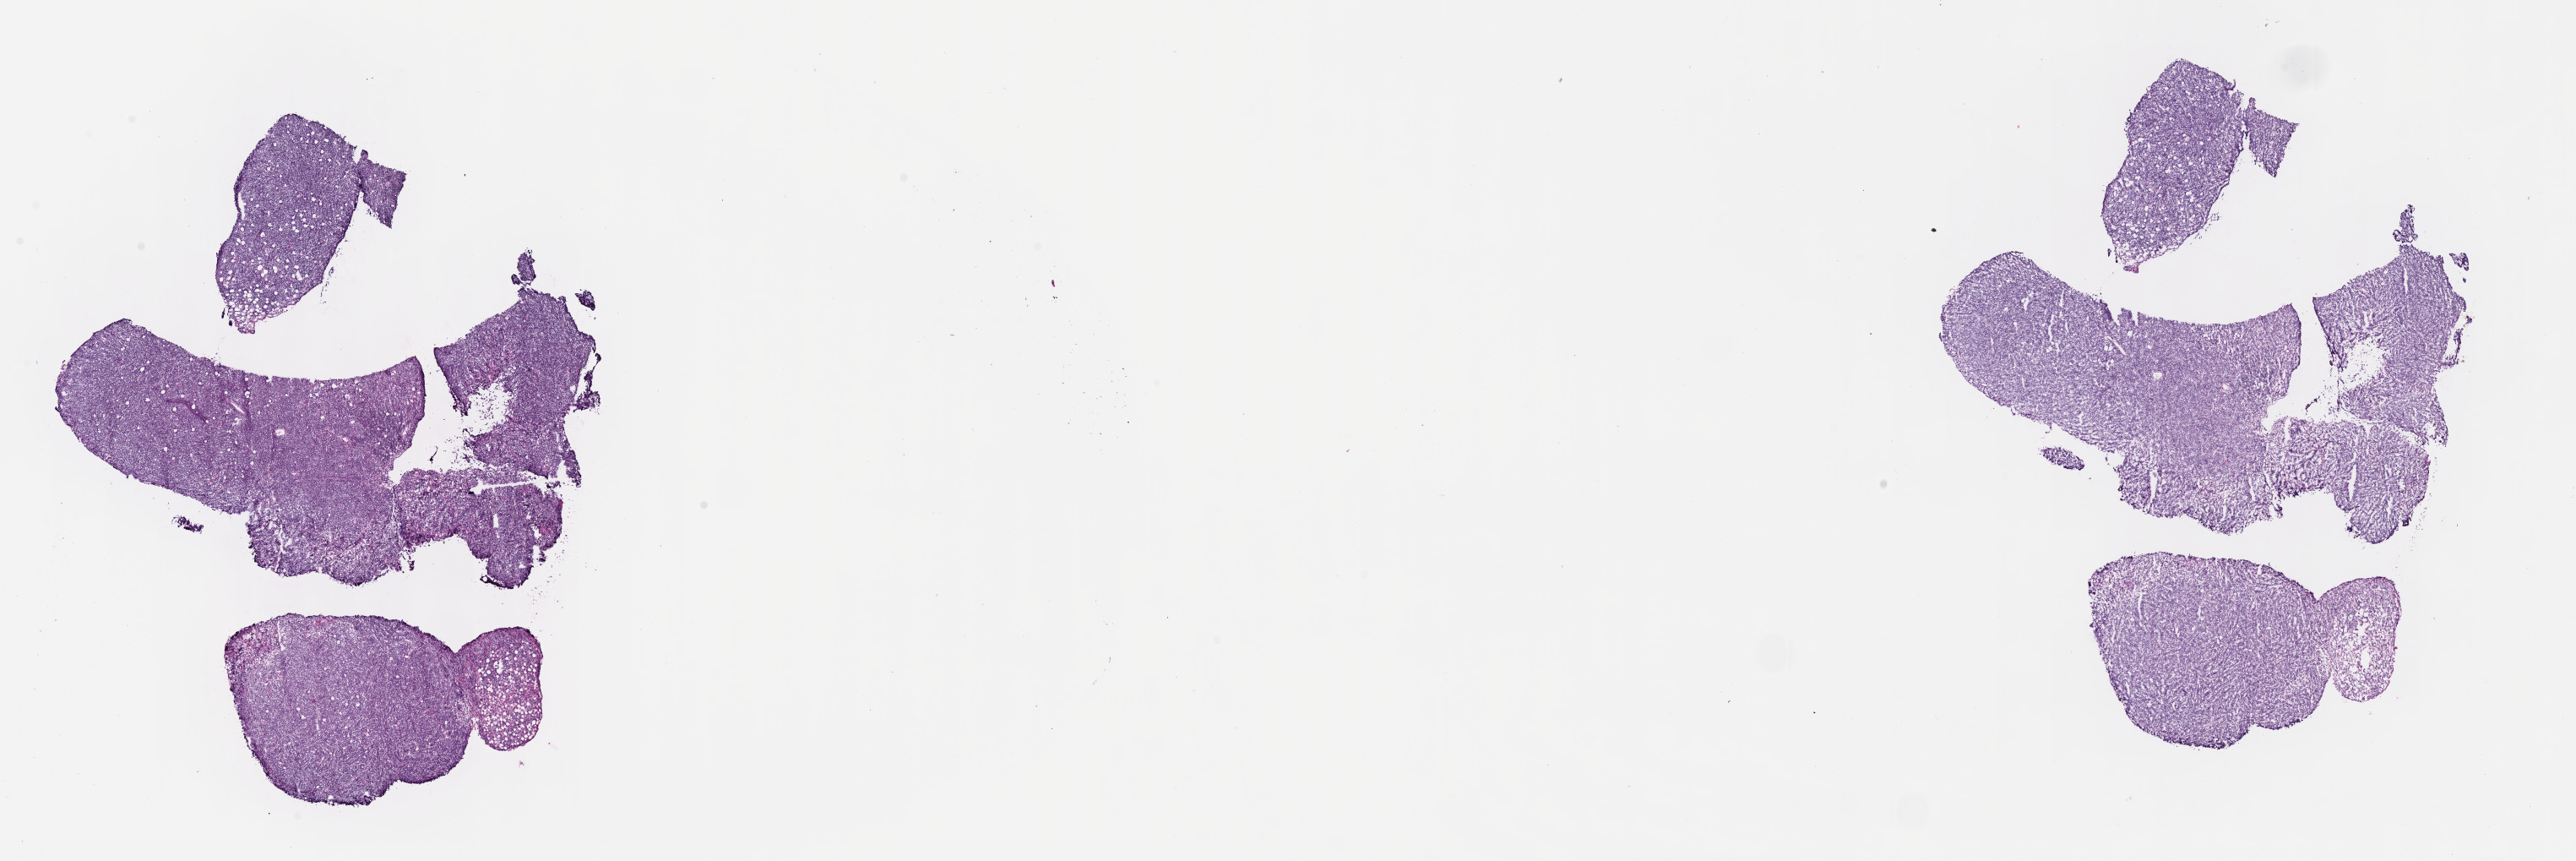
Whole-slide image, hematoxylin and eosin (H&E) stain, shown as a low-resolution overview of the whole scanned area (about 24.7 x 8.2 mm). Cryosection. Specimen: primary tumor. Site: peritoneum. Patient: male, age at initial diagnosis 9 years. Composition of this section per pathologist review: tumor cells 90%, tumor nuclei 95%, stromal cells 5%, necrosis 5%, normal cells 0%. Inflammatory infiltration, as recorded: lymphocyte infiltration 3%, monocyte infiltration 3%, neutrophil infiltration 0%.
* diagnosis: Burkitt lymphoma, NOS
* Ann Arbor stage (patient): Stage III